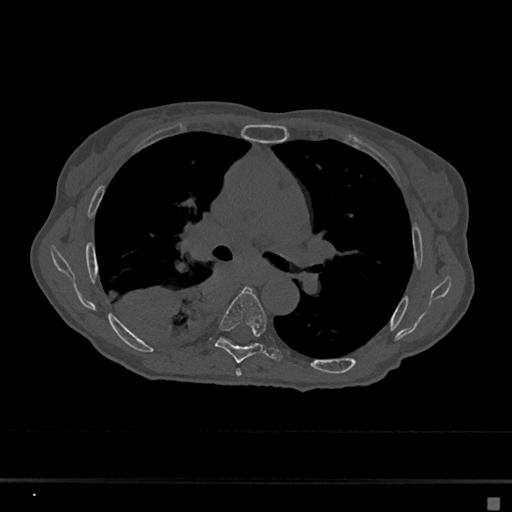
CT including the spine, one axial slice; reconstruction kernel Br40s/3; bone window (W 1800 / L 400 HU); 512 × 512 image matrix. Patient: female, 68 years. Case-level facts recorded for this patient, not image findings: primary cancer: renal.
Annotated regions visible in this slice (semi-automatic segmentation, software-assisted and operator-edited):
- T5 vertebra: box from (x=235, y=369) to (x=242, y=376) px
- T6 vertebra: (x=215, y=287)–(x=282, y=363)